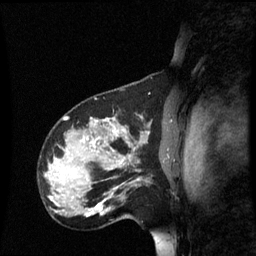
Breast MRI (dynamic contrast-enhanced), one sagittal slice; slice 46 of 60 in the series (ordered by position); dynamic contrast-enhanced series, image 2 of 3 at this slice position (ordered by acquisition); 1.5 T; TE 4.2 ms, TR 8.9 ms; 2.2 mm slice thickness; 256 × 256 image matrix, field of view 220 × 220 mm. Patient: female, 31 years. Case-level facts recorded for this patient, not image findings: setting: breast cancer imaged before/during neoadjuvant chemotherapy; receptor status: HR-positive, HER2-negative.
Annotated regions visible in this slice (semi-automatically segmented with operator editing):
- analysis volume of interest (the breast-tissue region the enhancement analysis was run in; not a lesion): bounding box <90,180,138,223> (left, top, right, bottom; pixels)
- tumour enhancement mask (voxels above the 70 % enhancement threshold inside the analysis volume of interest): <90,204,105,217>